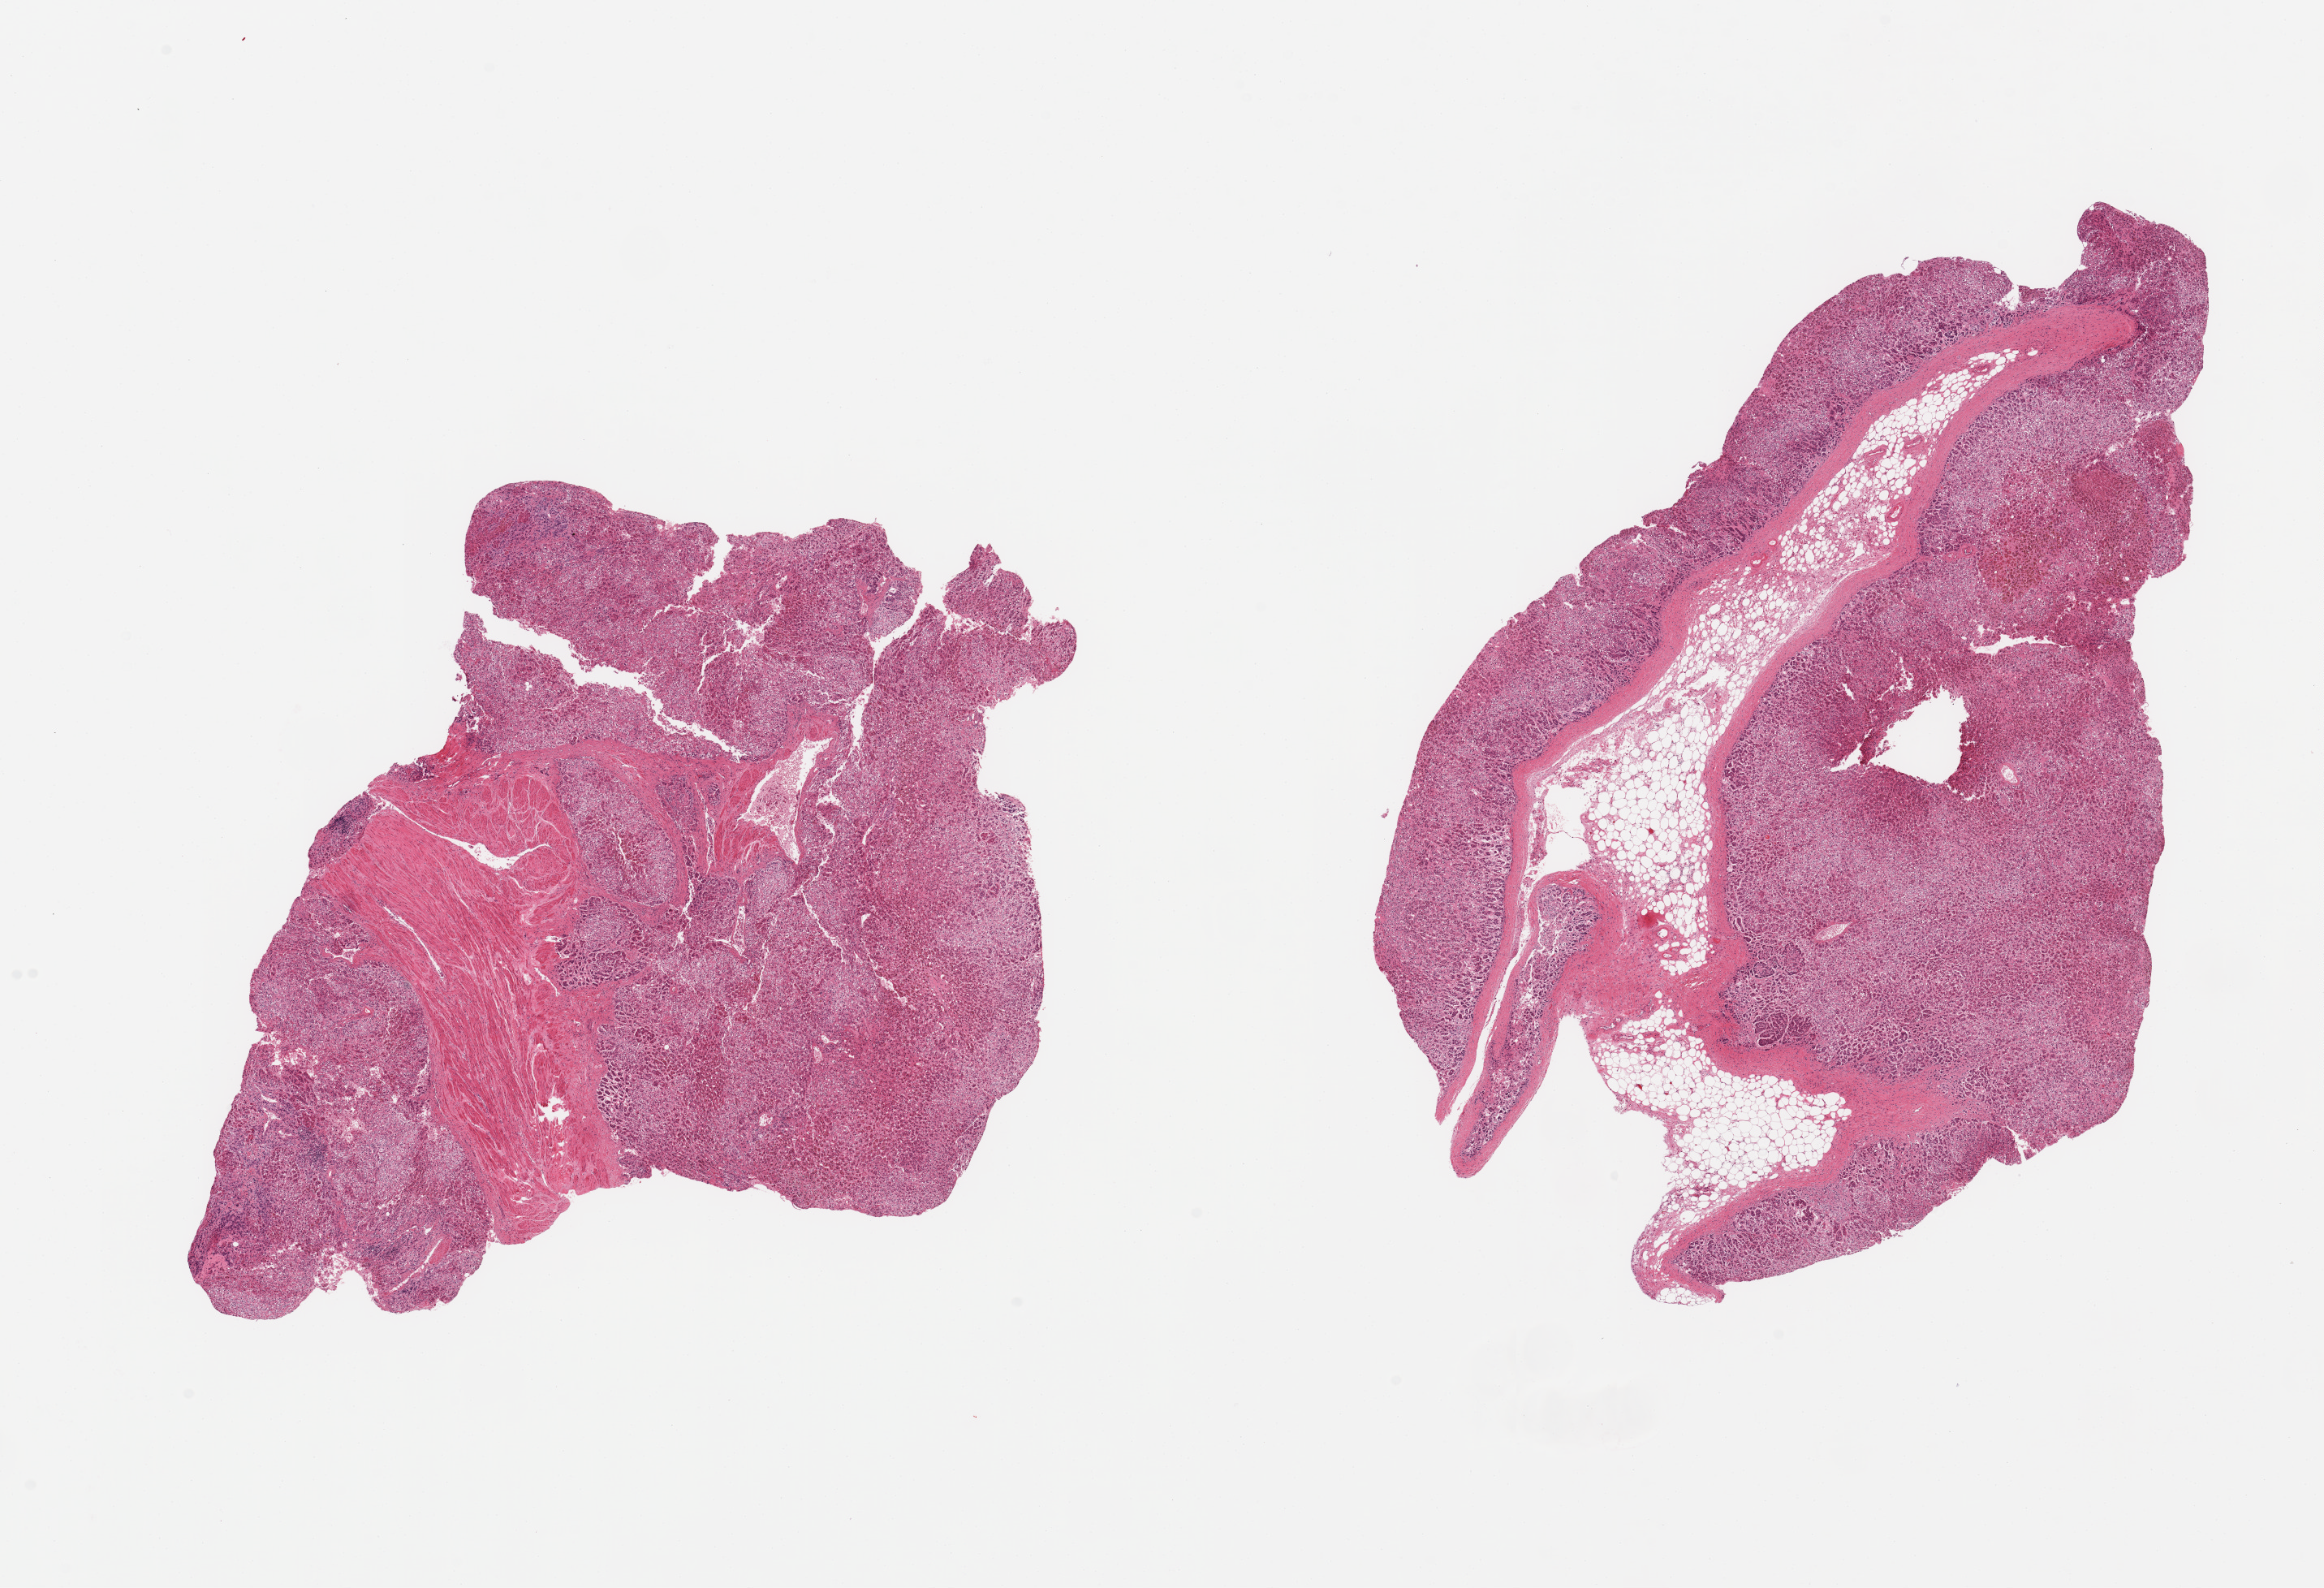
Whole-slide image, hematoxylin and eosin (H&E) stain, a low-resolution overview of the entire scanned area, about 22.6 x 15.5 mm (acquisition: 20x scan). PAXgene-fixed, paraffin-embedded tissue. Sampled site (target tissue): adrenal gland. Donor tissue sample. Donor: male.
- reviewer comment on this tissue sample: 2 pieces, ~all cortex, ~20-25% adherent fat/fibromuscular tissue